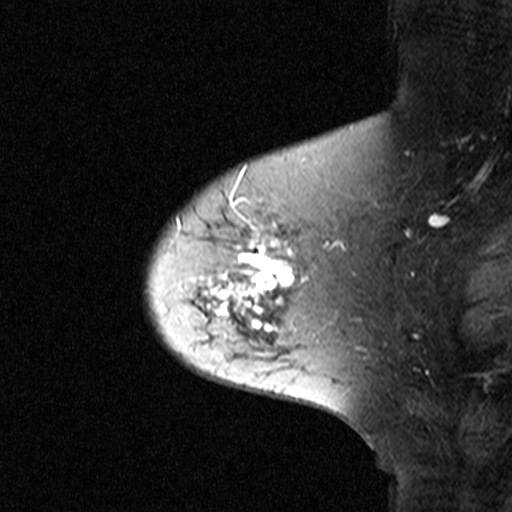
Breast MRI (dynamic contrast-enhanced), one sagittal slice; slice 34 of 44 in the series (ordered by position); dynamic contrast-enhanced study with each time point stored as its own series, time point 2 of 3 at this slice position (early post-contrast, ordered by acquisition time); 1.5 T; TE 4.5 ms, TR 11 ms; 3 mm slice thickness; 512 × 512 image matrix, field of view 200 × 200 mm. Patient: female, 65 years. Case-level facts recorded for this patient, not image findings: setting: breast cancer imaged before/during neoadjuvant chemotherapy; receptor status: HER2-positive.
Outlined on this slice (semi-automatic segmentation, software-assisted and operator-edited):
- analysis volume of interest (the breast-tissue region the enhancement analysis was run in; not a lesion): box from (x=160, y=172) to (x=329, y=345) px
- tumour enhancement mask (voxels above the 90 % enhancement threshold inside the analysis volume of interest): (x=201, y=174)–(x=293, y=332)